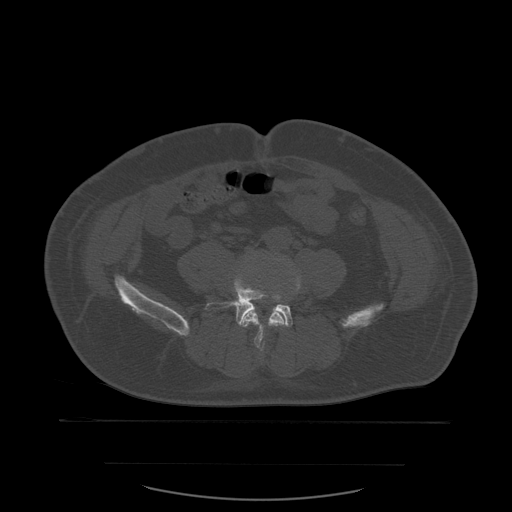
CT including the spine, one axial slice; position 150 of 590 along the scan axis; bone window (W 1800 / L 400 HU); 1.25 mm slice thickness; 512 × 512 image matrix. Patient age 71 years. Case-level facts recorded for this patient, not image findings: primary cancer: lung.
Annotated regions visible in this slice (semi-automatically segmented with operator editing):
- L4 vertebra: box from (x=243, y=264) to (x=301, y=350) px
- L5 vertebra: (x=205, y=275)–(x=293, y=327)